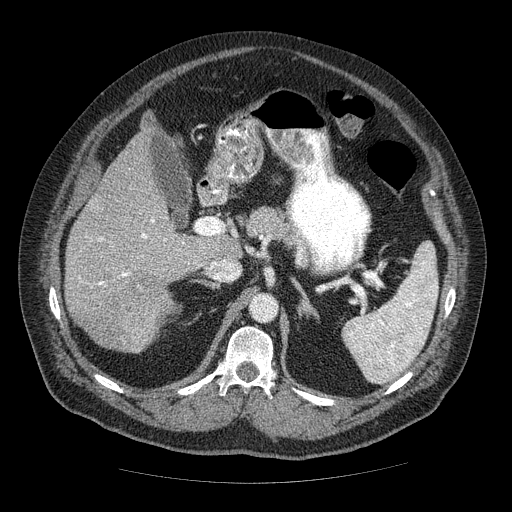
Contrast-enhanced abdominal CT (liver protocol), one axial slice. Slice 31 of 85 in the series (ordered by position). Reconstruction kernel STANDARD. 120 kVp. Soft-tissue window (W 400 / L 40 HU). 512 × 512 image matrix, field of view 420 × 420 mm. From the clinical record (not read from this slice): diagnosis: hepatocellular carcinoma (patient treated with transarterial chemoembolisation; whether this scan precedes or follows treatment is not stated here); TNM stage (as recorded): Stage-IIIA; Child-Pugh class: A; tumour nodularity: multinodular; tumour size: 7 cm.
Outlined on this slice (semi-automatic segmentation, software-assisted and operator-edited):
- liver parenchyma outside the tumour (the mass and vessels are separate outlines, so this box may not span the whole liver): bounding box <64,120,236,340> (left, top, right, bottom; pixels)
- mass: <87,273,175,353>
- liver vessels: <79,219,166,285>